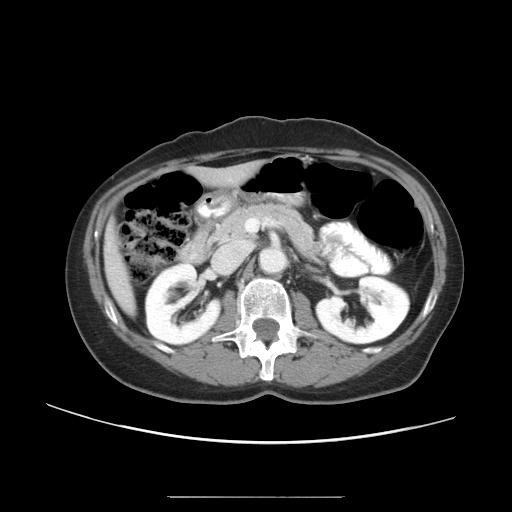
Contrast-enhanced abdominal CT, one axial slice. Reconstruction kernel STANDARD. 120 kVp. Intravenous contrast given. Soft-tissue window (W 400 / L 40 HU). 5 mm slice thickness. 512 × 512 image matrix, field of view 389 × 389 mm. Female patient, age 58 years. Case-level facts recorded for this patient, not image findings: diagnosis: colorectal cancer liver metastases, imaged before liver resection; multiple liver metastases: yes; largest metastasis: 7.3 cm; disease in both lobes: yes.
Outlined on this slice (outlined manually by an expert reader):
- liver: box from (x=107, y=168) to (x=251, y=310) px
- planned liver remnant (the part of the liver to remain after resection): (x=206, y=169)–(x=251, y=179)